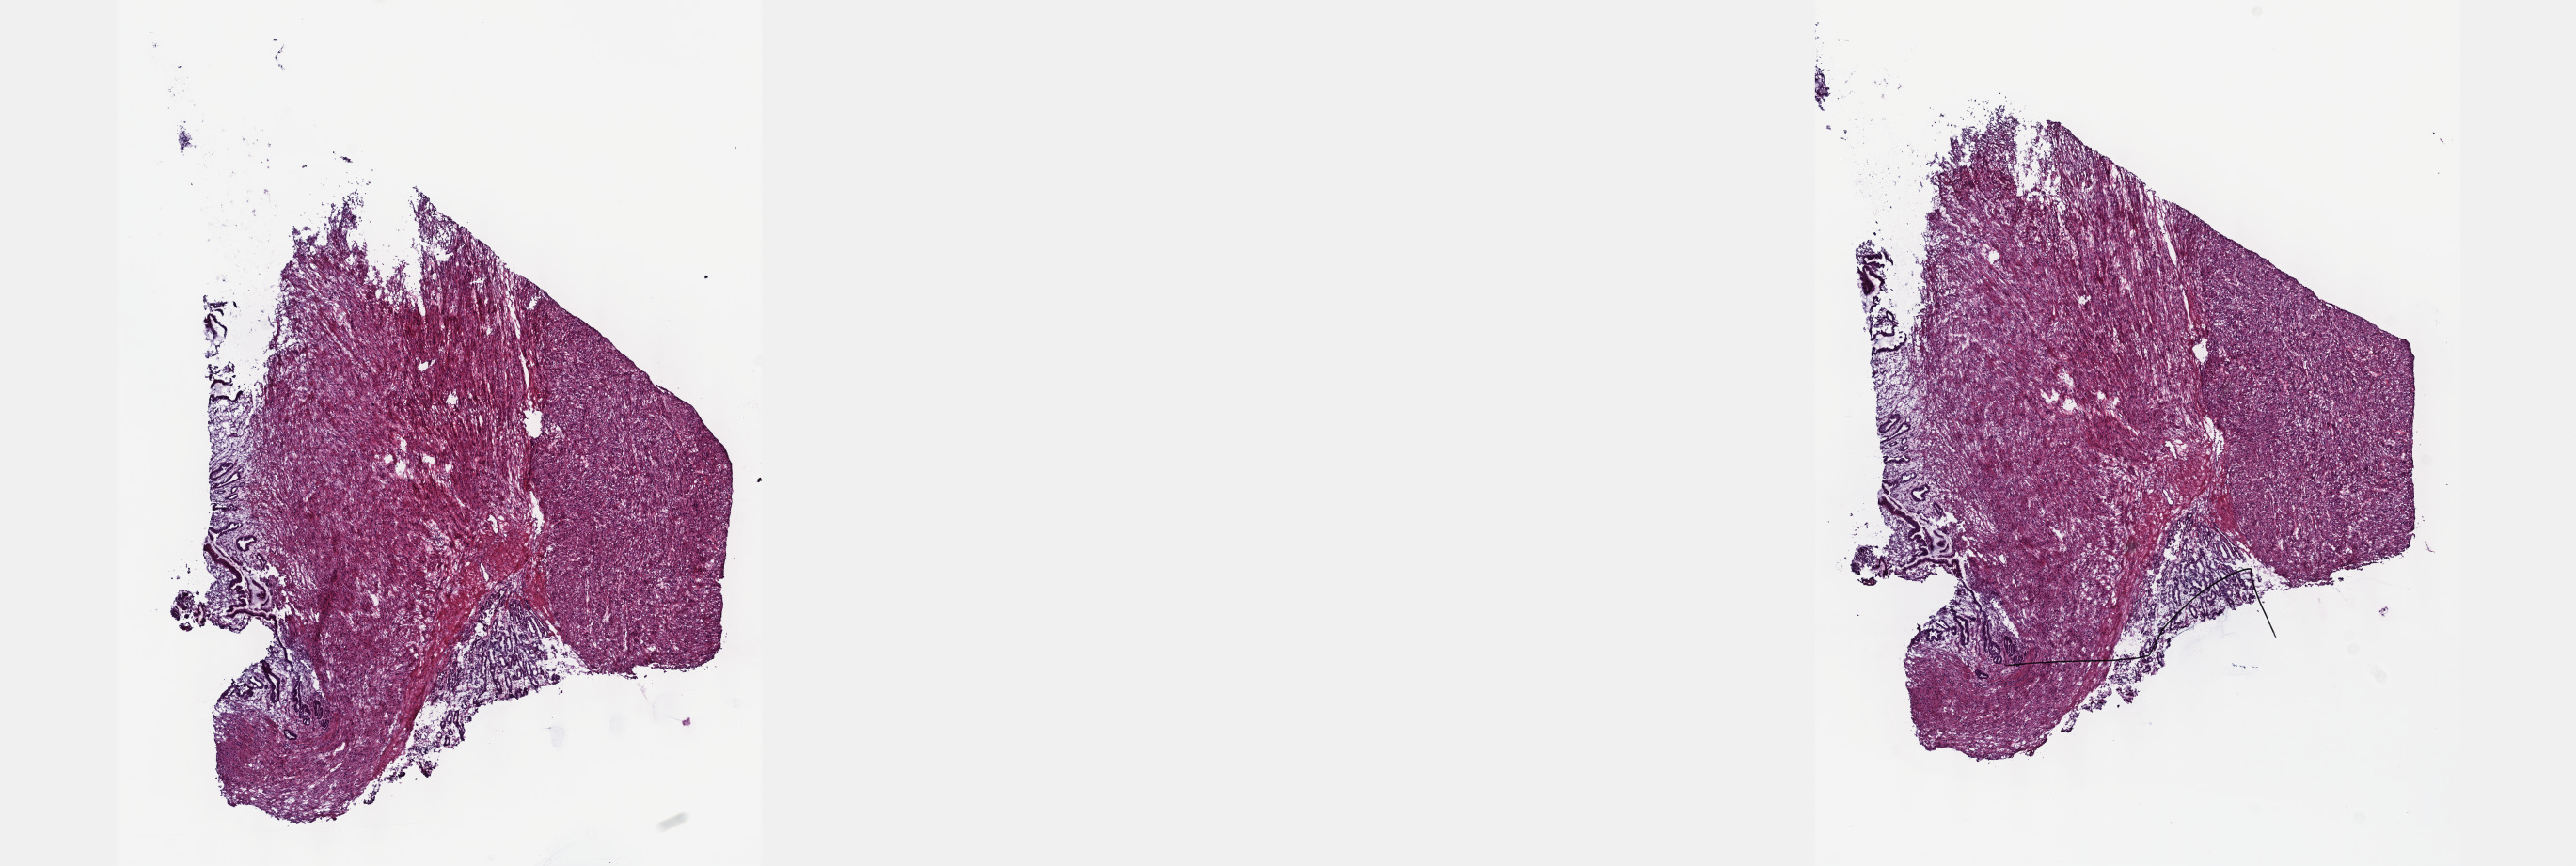
Digitized Hematoxylin and eosin (H&E) stained tissue section (whole slide), low-resolution overview of the scanned area, about 22.1 x 7.4 mm; frozen section from the top of the tissue portion; retroperitoneum and peritoneum, primary tumour sample. Male patient; age at initial diagnosis 62 years. Composition of this section per pathologist review: tumour cells 85%, tumour nuclei 75%, normal cells 15%, stromal cells 0%, necrosis 0%. Infiltration values recorded for this section: lymphocyte infiltration 2%, monocyte infiltration 0%, neutrophil infiltration 0%.
Pathologic diagnosis: Leiomyosarcoma, NOS (retroperitoneum).